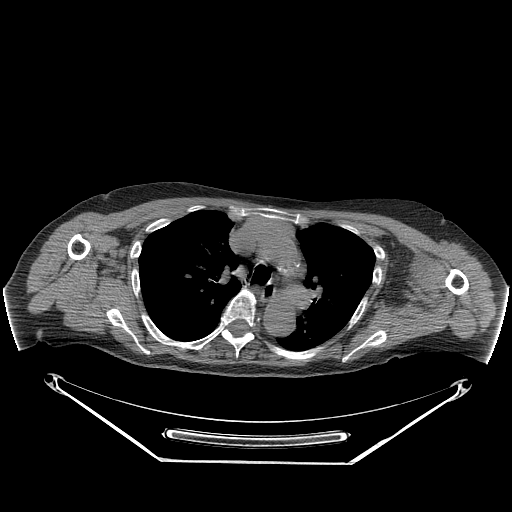
CT of an extremity soft-tissue mass (from a PET/CT study), one axial slice; position 187 of 267 along the scan axis; reconstruction kernel STANDARD; soft-tissue window (W 400 / L 40 HU); 3.75 mm slice thickness; 512 × 512 image matrix, field of view 500 × 500 mm. Female patient. Case-level facts recorded for this patient, not image findings: histological type: pleiomorphic leiomyosarcoma; grade: high; site of the primary tumour: left biceps.
Outlined on this slice (expert contour drawn on MRI and transferred to this co-registered scan by the dataset authors):
- gross tumour volume including surrounding oedema: bounding box <413,258,437,300> (left, top, right, bottom; pixels)